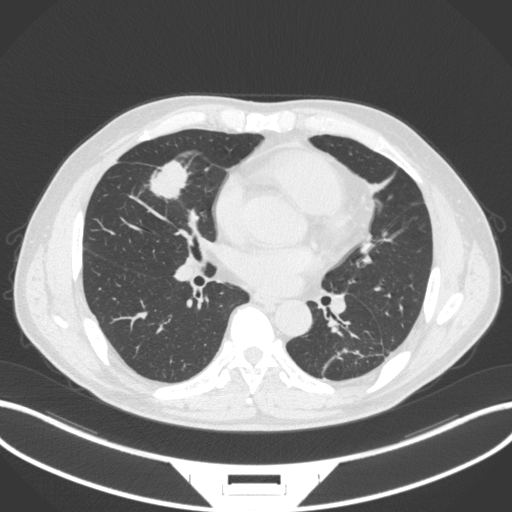
Chest CT, one axial slice. Position 141 of 399 along the scan axis. Reconstruction kernel B31f. 120 kVp. Lung window (W 1500 / L -600 HU). 1 mm slice thickness. 512 × 512 image matrix, field of view 400 × 400 mm. Patient: male, 59 years. From the clinical record (not read from this slice): clinical TNM (as recorded): T2a N1 M0.
Outlined on this slice (rectangle marked by the reading radiologist):
- lung tumour (recorded histology: adenocarcinoma): bounding box <147,157,193,204> (left, top, right, bottom; pixels)